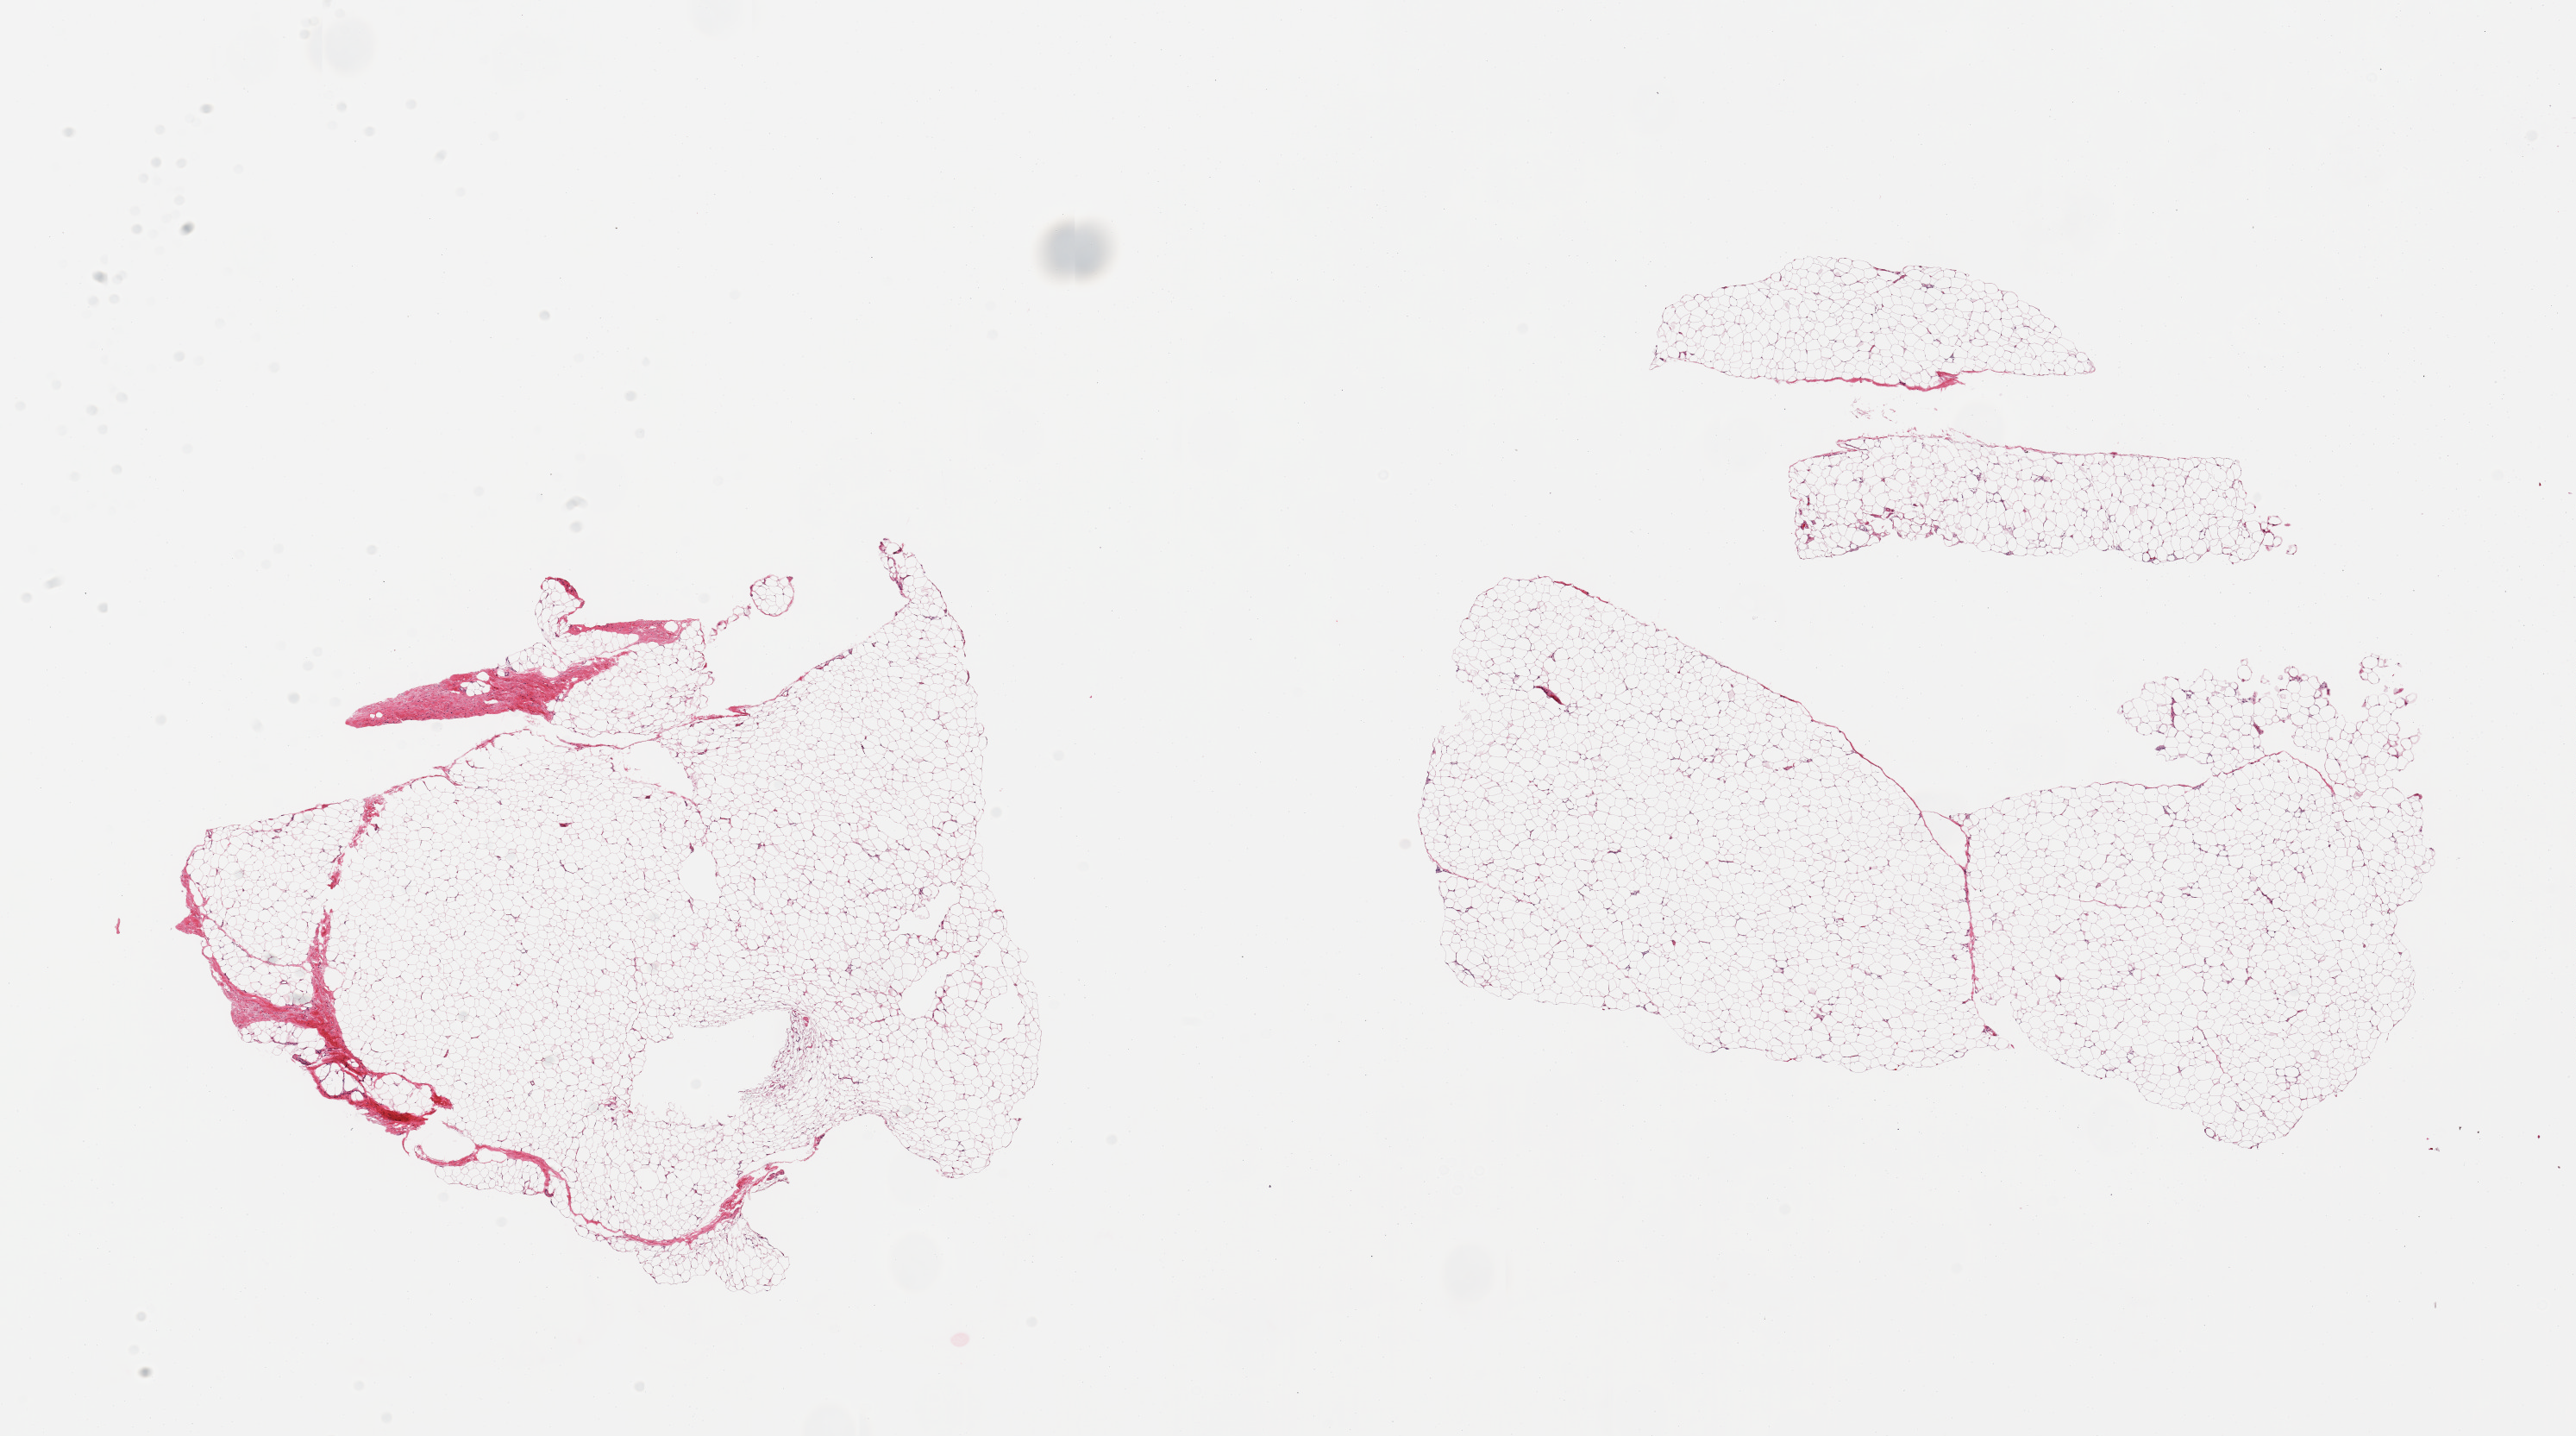
Whole-slide image, H&E stain — whole scanned area (about 23.6 x 13.2 mm) shown as a low-resolution overview, PAXgene-fixed, paraffin-embedded tissue, section of adipose tissue (target tissue), tissue donor sample.
- reviewer comment on this tissue sample: 2 pieces; minimal fibrous content